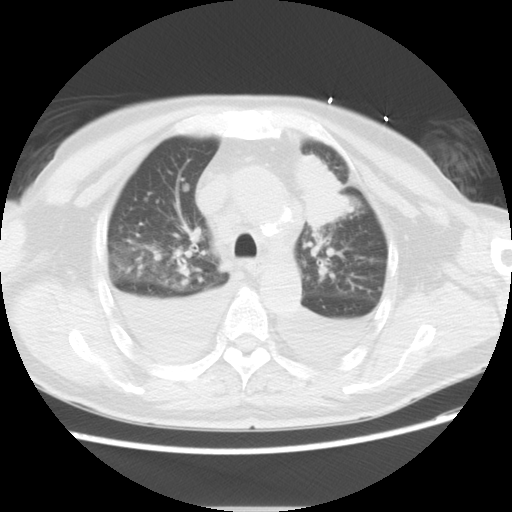
Chest CT, one axial slice. Position 19 of 21 along the scan axis. Reconstruction kernel STANDARD. 120 kVp. Lung window (W 1500 / L -600 HU). 5 mm slice thickness. 512 × 512 image matrix, field of view 350 × 350 mm. Male patient, age 66 years. Case-level facts recorded for this patient, not image findings: clinical TNM (as recorded): T1c N0 M0.
Structures marked on this image (rectangle marked by the reading radiologist):
- lung tumour (recorded histology: adenocarcinoma): box from (x=290, y=151) to (x=357, y=233) px